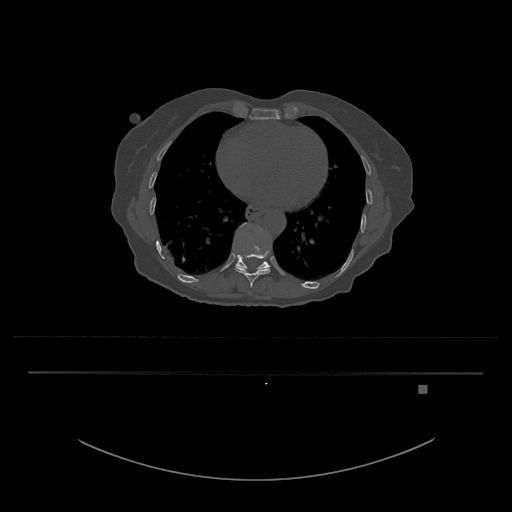
CT including the spine, one axial slice. Position 697 of 797 along the scan axis. Bone window (W 1800 / L 400 HU). 0.5 mm slice thickness. 512 × 512 image matrix, field of view 500 × 500 mm. Patient: female, 57 years. Case-level facts recorded for this patient, not image findings: primary cancer: cervical.
Outlined on this slice (semi-automatic segmentation, software-assisted and operator-edited):
- T10 vertebra: box from (x=235, y=246) to (x=270, y=288) px
- T11 vertebra: (x=233, y=223)–(x=271, y=269)